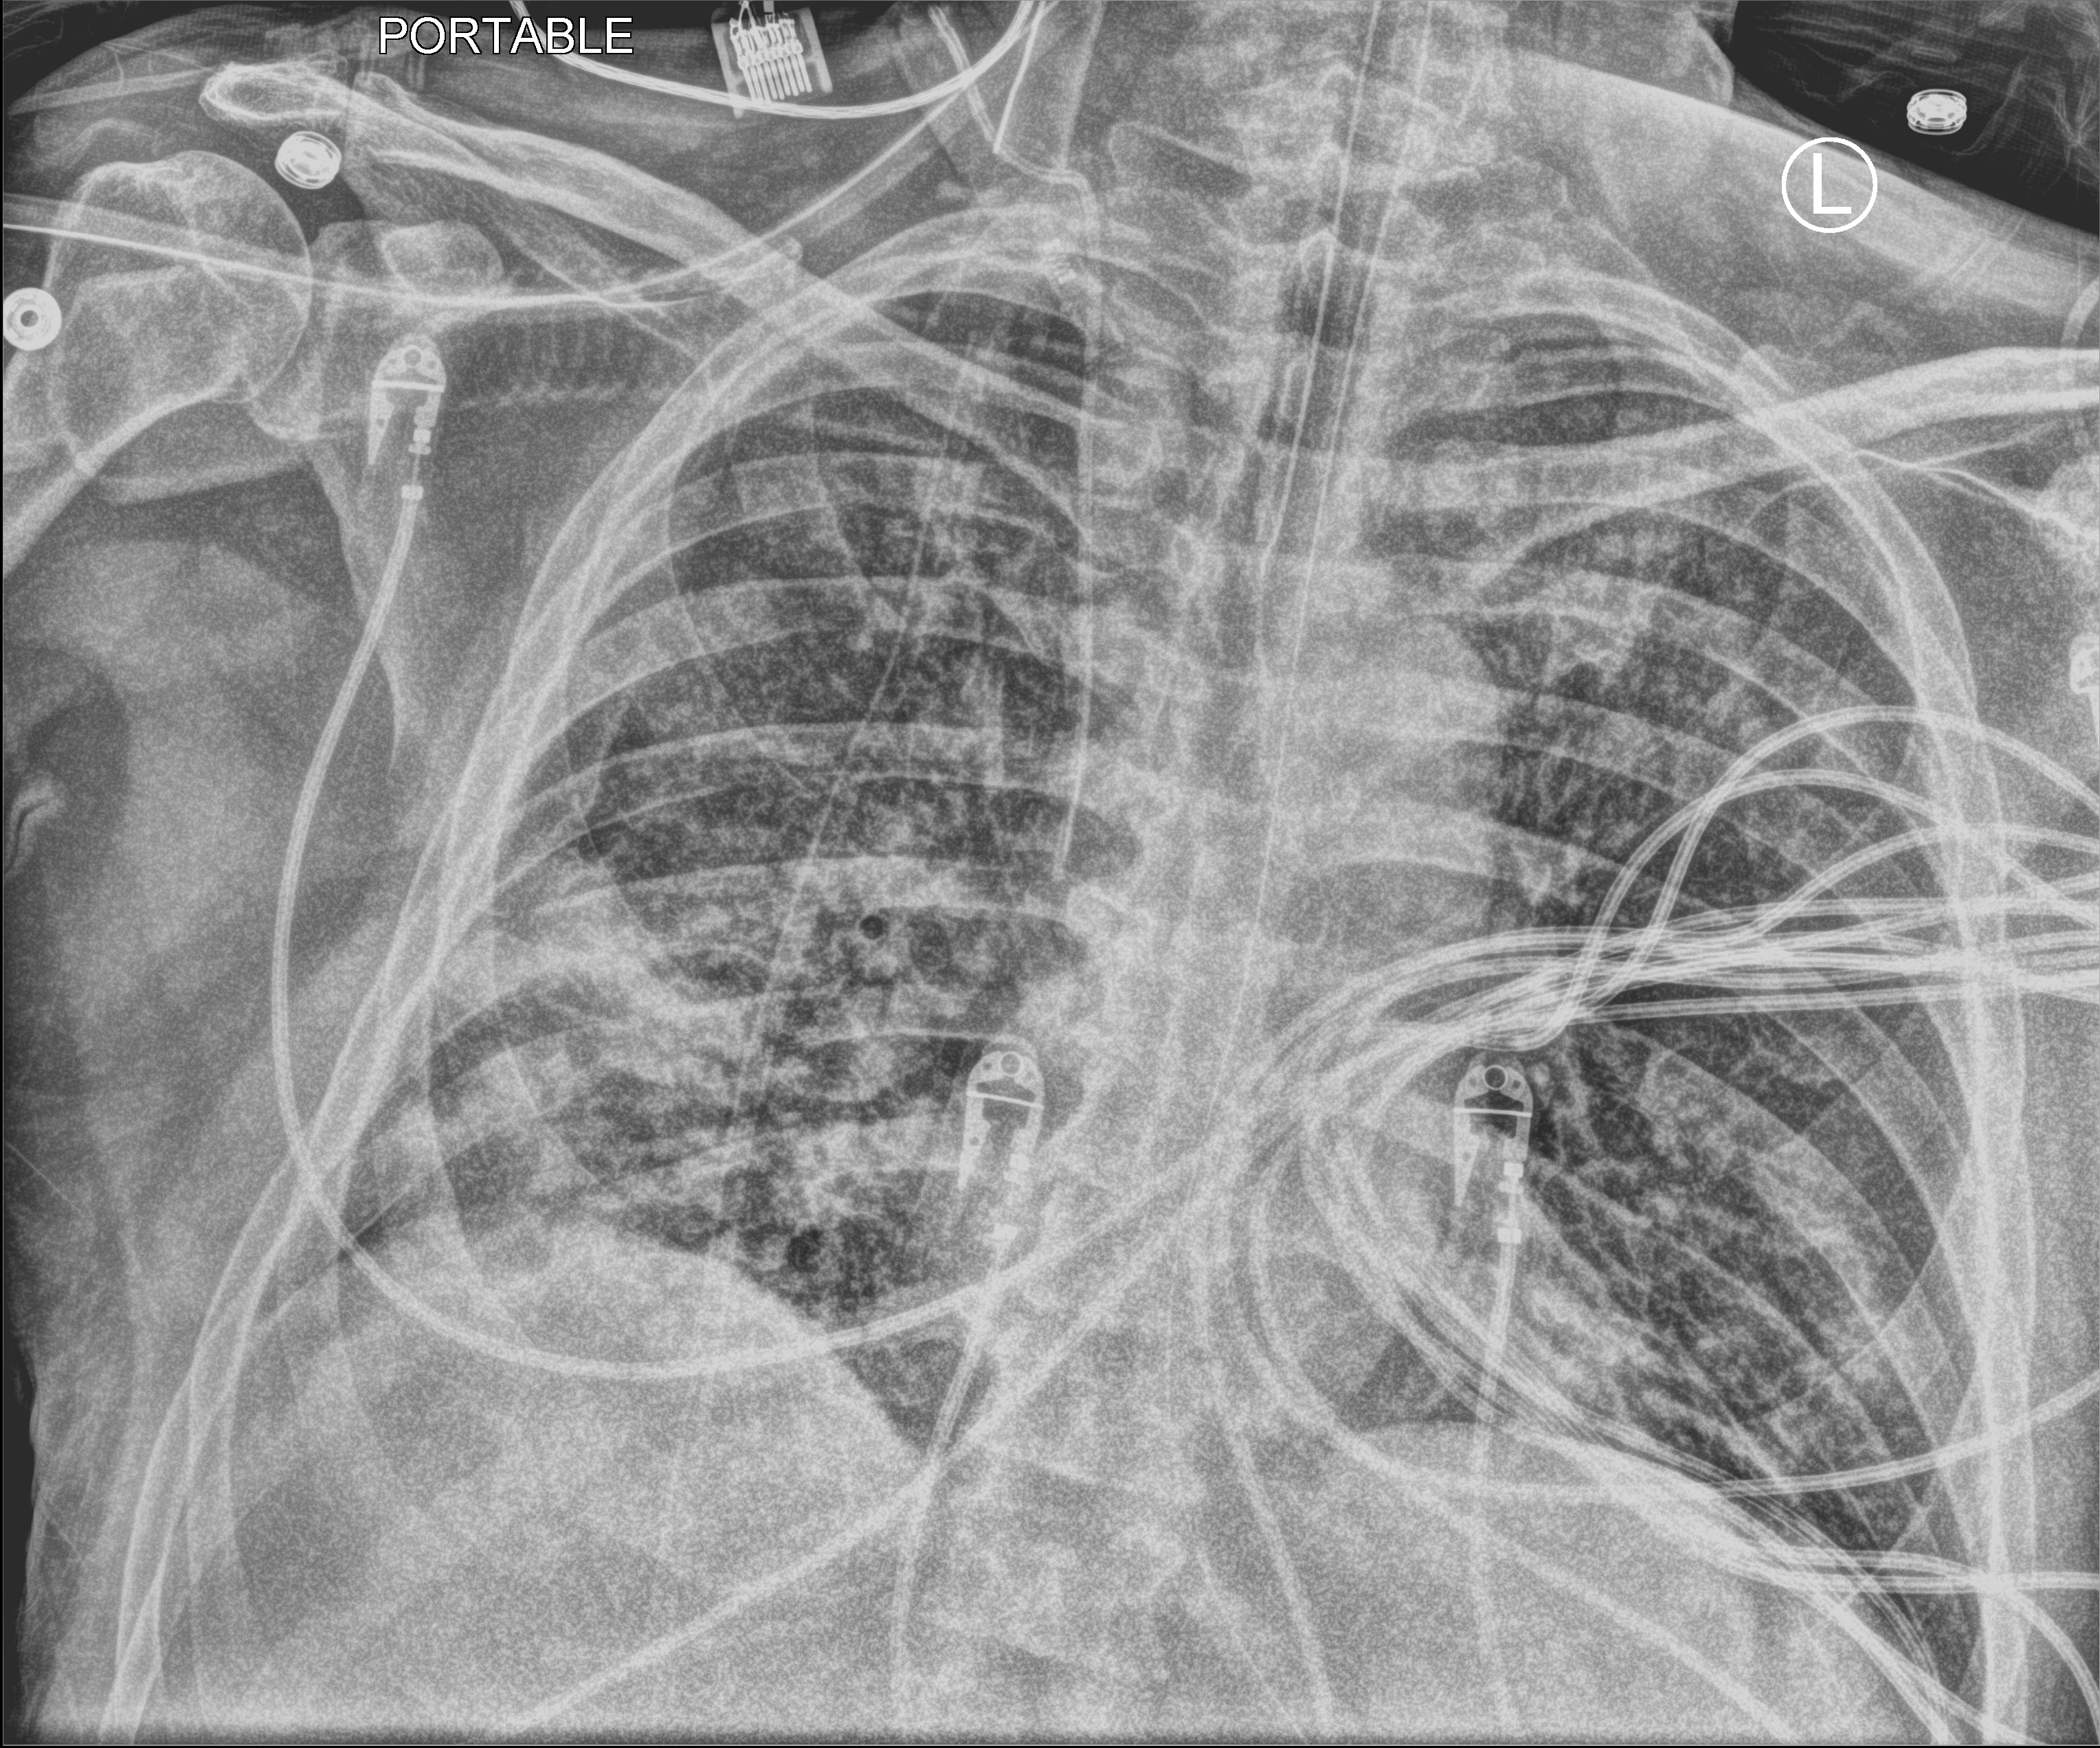
Chest X-ray (portable). Male patient hospitalised with COVID-19, age 60–74 years.
Hospital-stay facts (about this admission, not read from this image; timing relative to this image not recorded): mechanically ventilated during this hospital stay: yes; length of hospital stay: 33 days; admitted to intensive care during this hospital stay: yes.